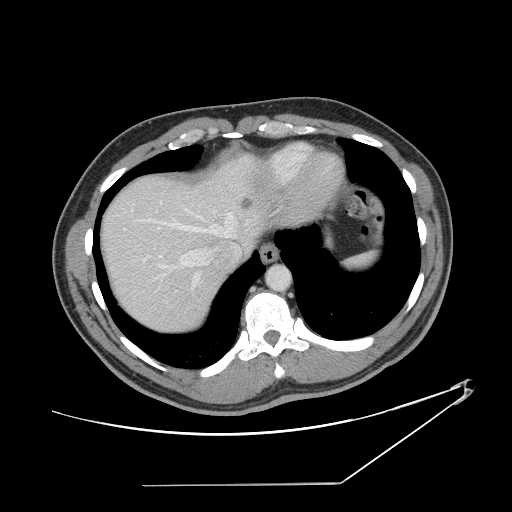
Contrast-enhanced abdominal CT, one axial slice; slice 125 of 152 in the series (ordered by position); soft-tissue window (W 400 / L 40 HU); 512 × 512 image matrix, field of view 432 × 432 mm. Male patient, age 45 years. Case-level facts recorded for this patient, not image findings: diagnosis: colorectal cancer liver metastases, imaged before liver resection; multiple liver metastases: no; largest metastasis: 1 cm; disease in both lobes: no.
Outlined on this slice (manually delineated by an expert):
- hepatic veins: bounding box (x1, y1, x2, y2) in pixels: (123, 201, 236, 289)
- liver: (103, 158, 264, 332)
- planned liver remnant (the part of the liver to remain after resection): (103, 177, 234, 331)
- portal vein (with intrahepatic branches): (159, 255, 162, 258)
- liver metastasis: (240, 196, 255, 211)